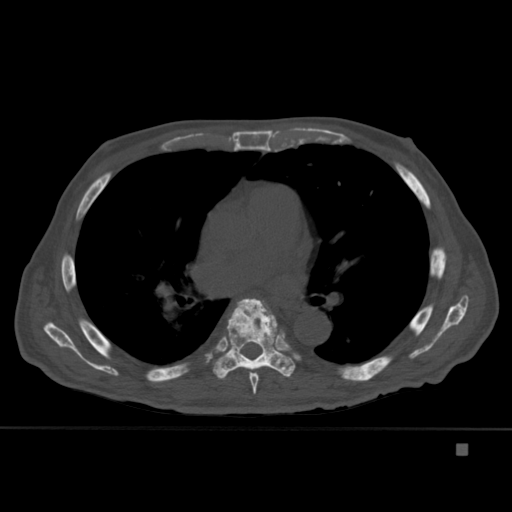
CT including the spine, one axial slice; position 283 of 451 along the scan axis; bone window (W 1800 / L 400 HU); 1.5 mm slice thickness; 512 × 512 image matrix. Male patient, age 75 years. From the clinical record (not read from this slice): primary cancer: prostate.
Structures marked on this image (semi-automatic segmentation, software-assisted and operator-edited):
- T4 vertebra: bounding box <270,321,284,338> (left, top, right, bottom; pixels)
- T6 vertebra: <249,303,269,394>
- T7 vertebra: <213,298,296,380>